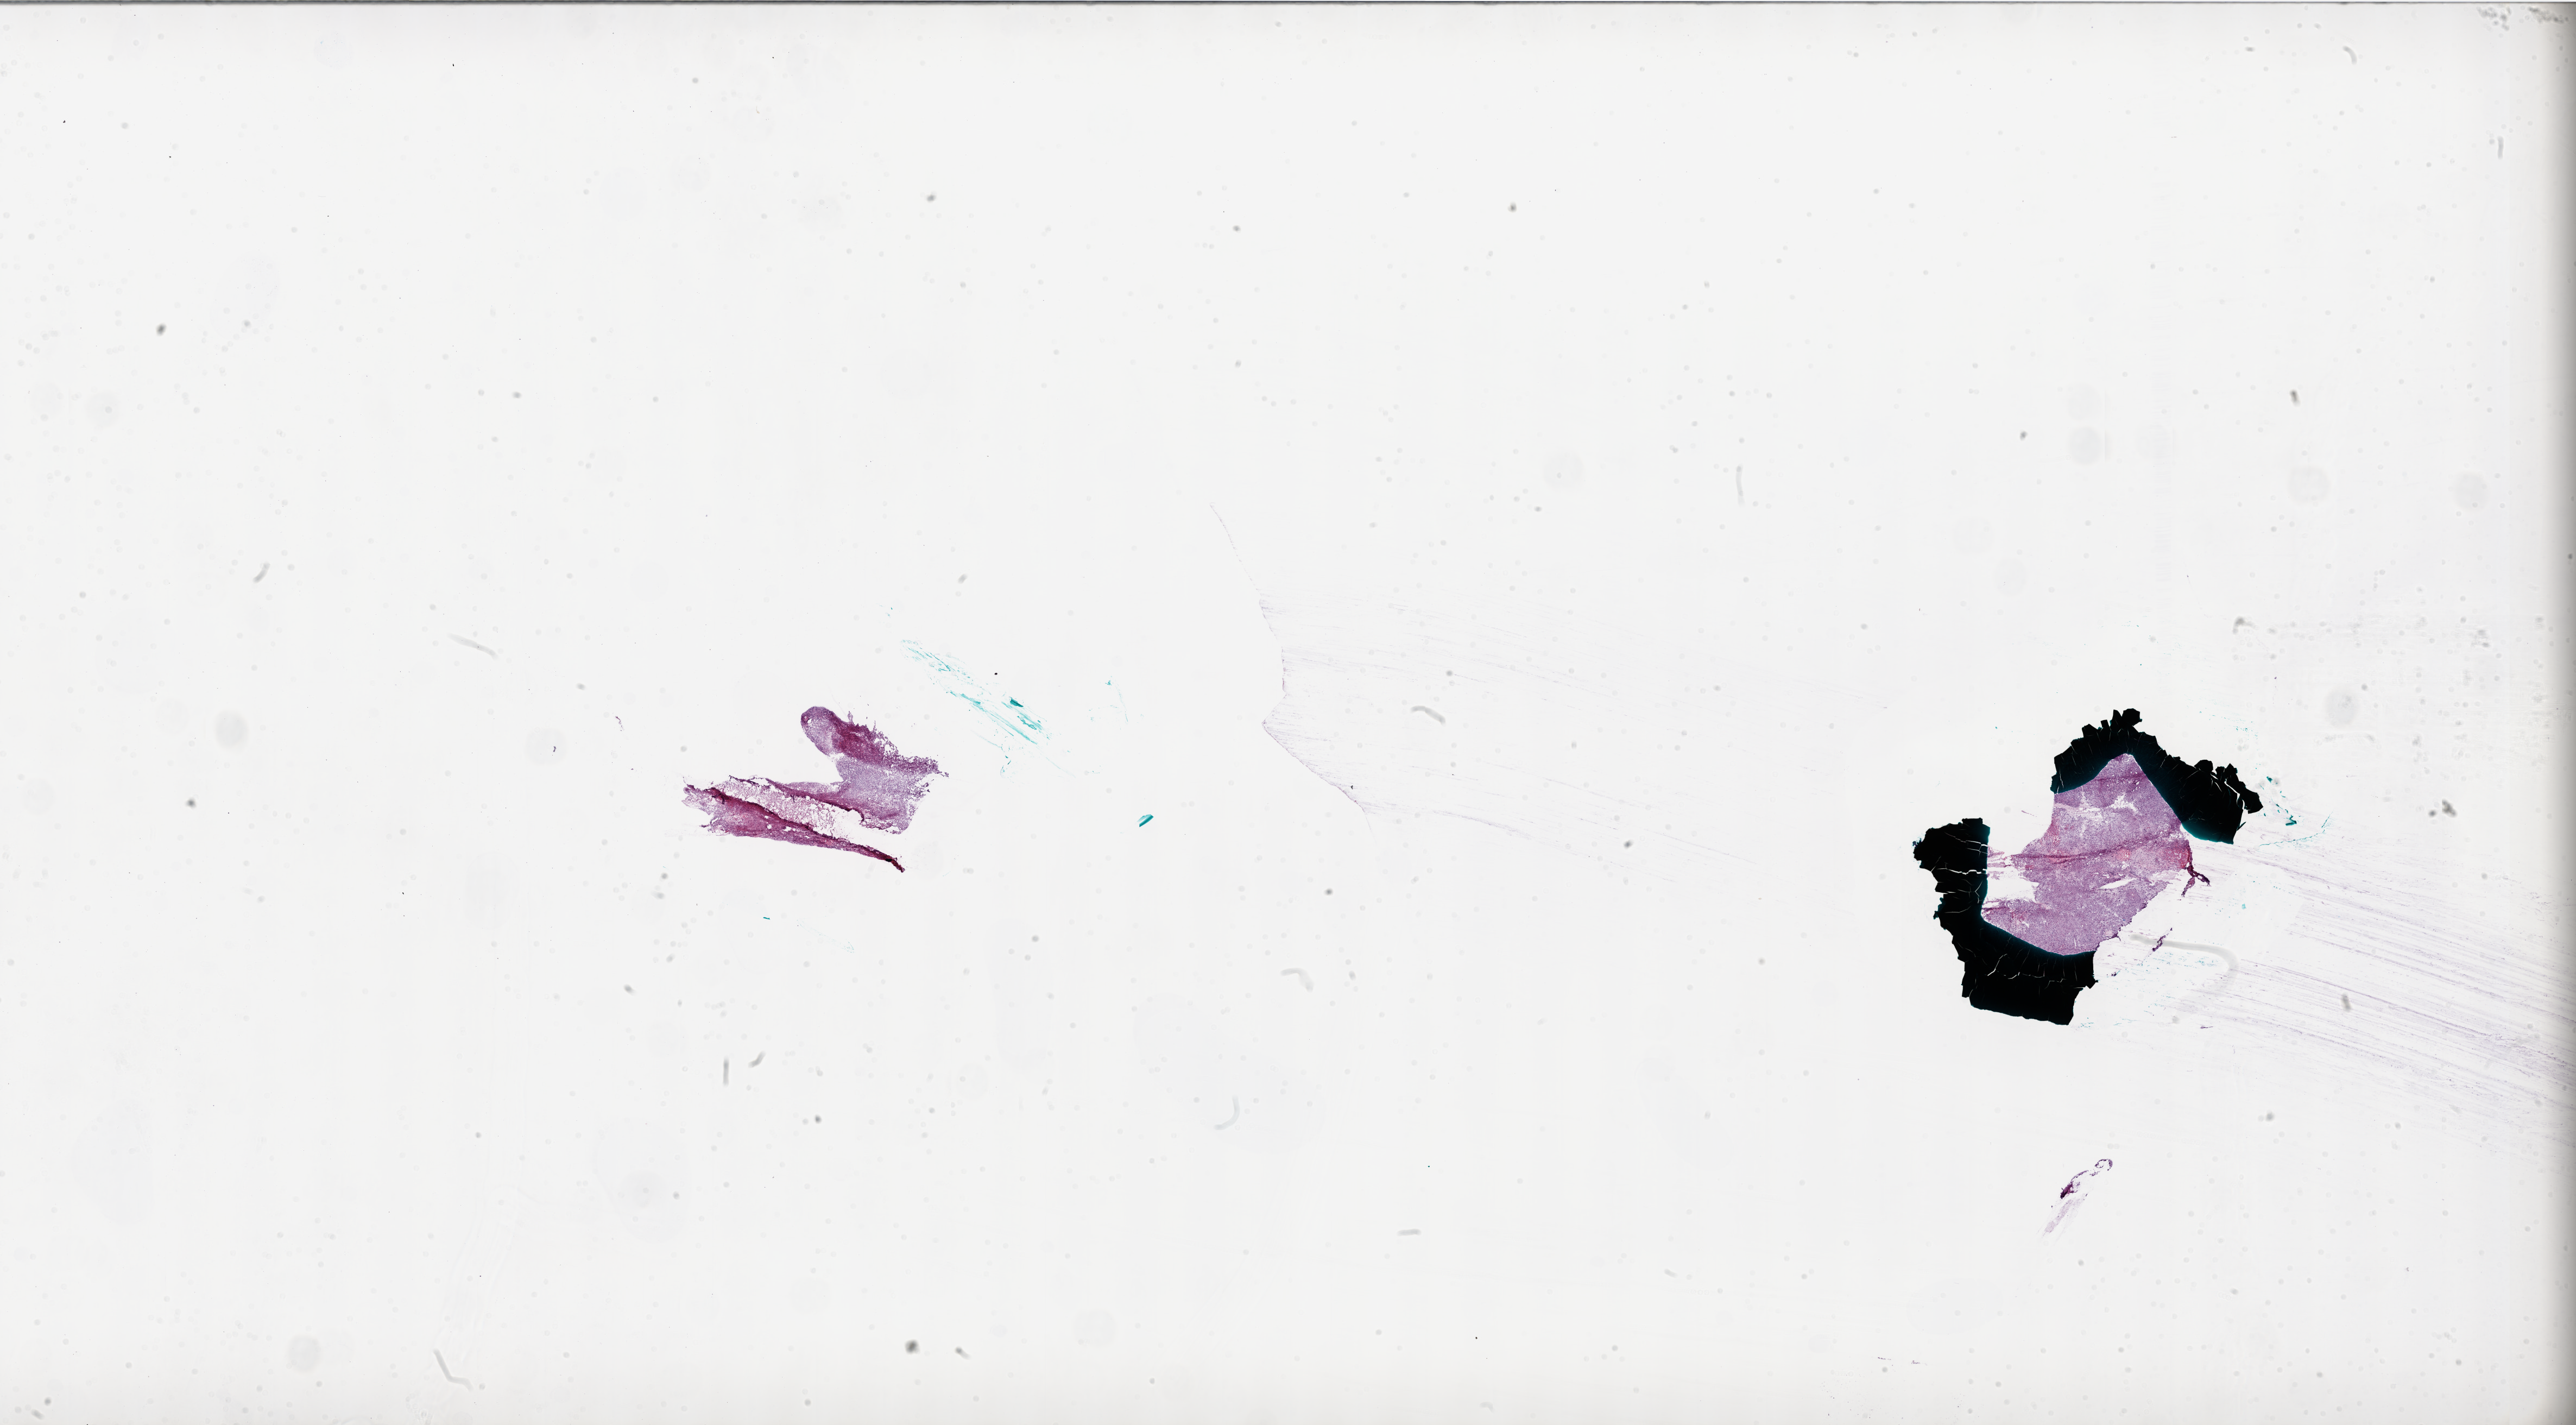
Digitized Hematoxylin and eosin (H&E) stained tissue section (whole slide) — whole scanned area (about 38.0 x 21.0 mm) shown as a low-resolution overview; frozen section from the bottom of the tissue portion; brain, primary tumour sample. Patient: female, age at initial diagnosis 37 years. Pathologist review of this section (percent, as recorded): tumour cells 98%, tumour nuclei 98%, normal cells 0%, stromal cells 0%, necrosis 2%. Inflammatory infiltration, as recorded: neutrophil infiltration 2%.
Histologic diagnosis: Glioblastoma.